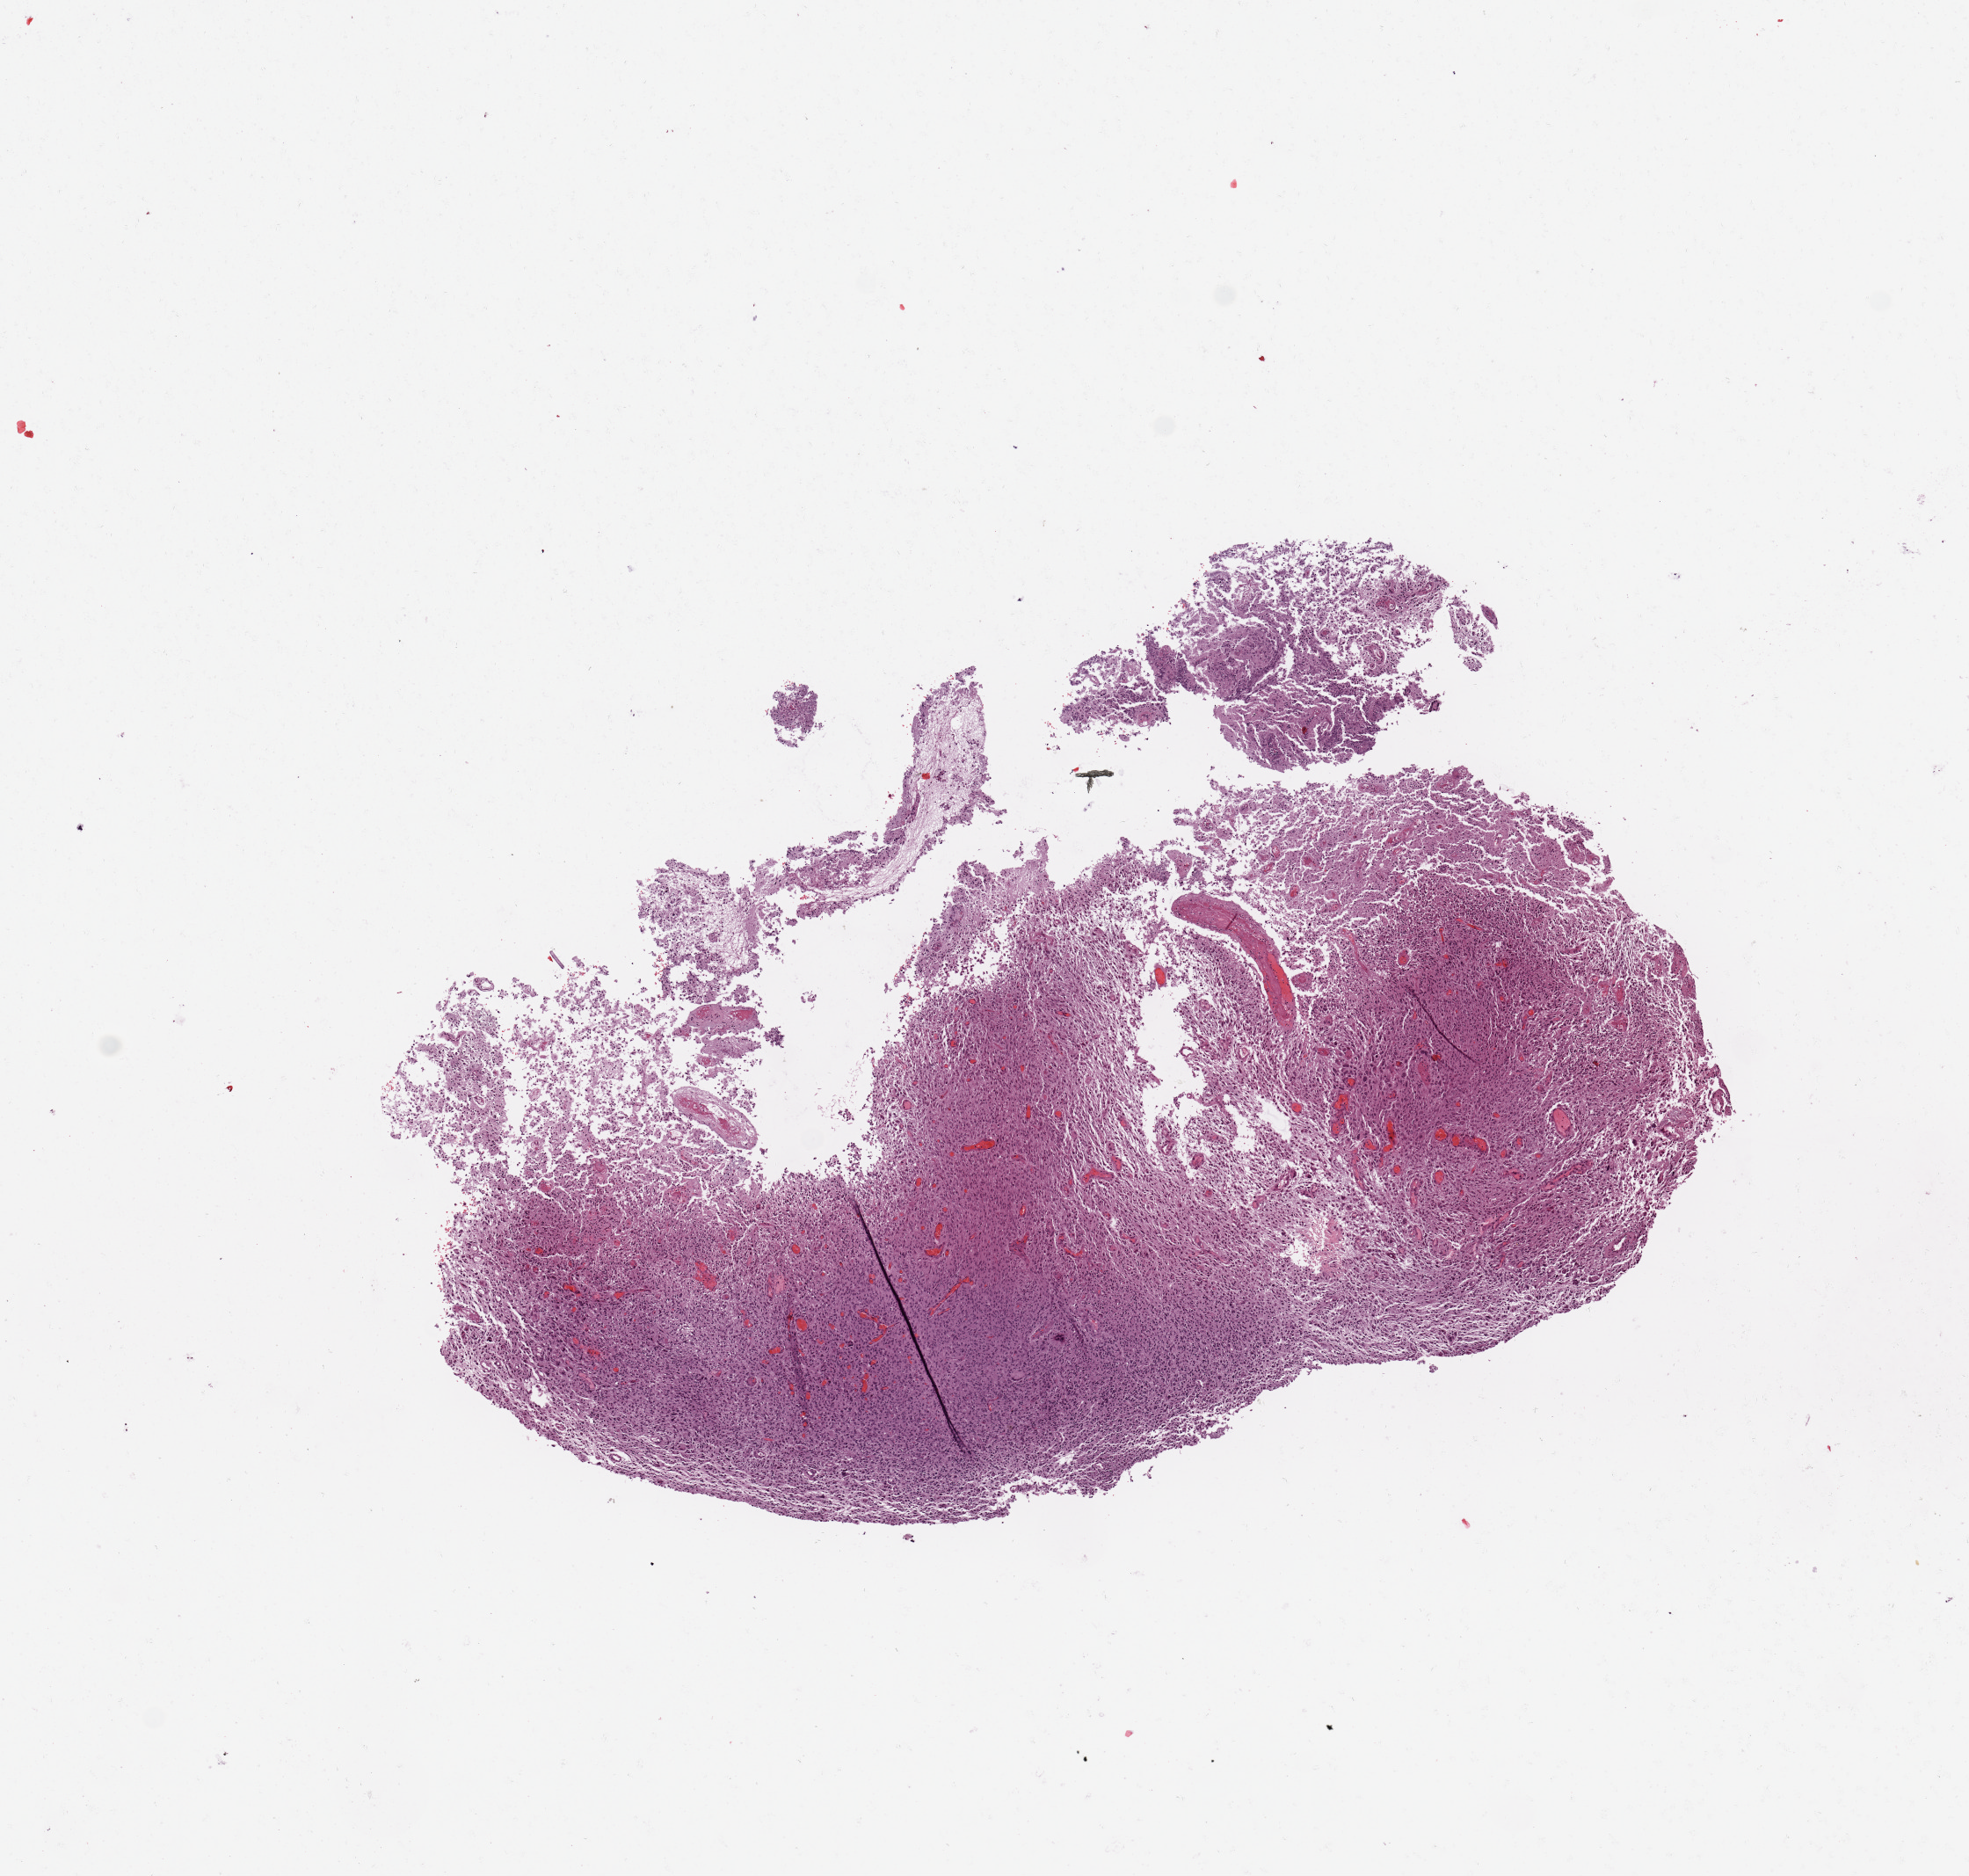
Whole-slide histology image, Hematoxylin and eosin (H&E) stained, a low-resolution overview of the entire scanned area, about 8.9 x 8.4 mm (from a 20x scan). Tumour tissue sample, brain. Patient: female, age 72 years.
• histologic diagnosis: Glioblastoma
• primary tumour site (as recorded): temporal lobe